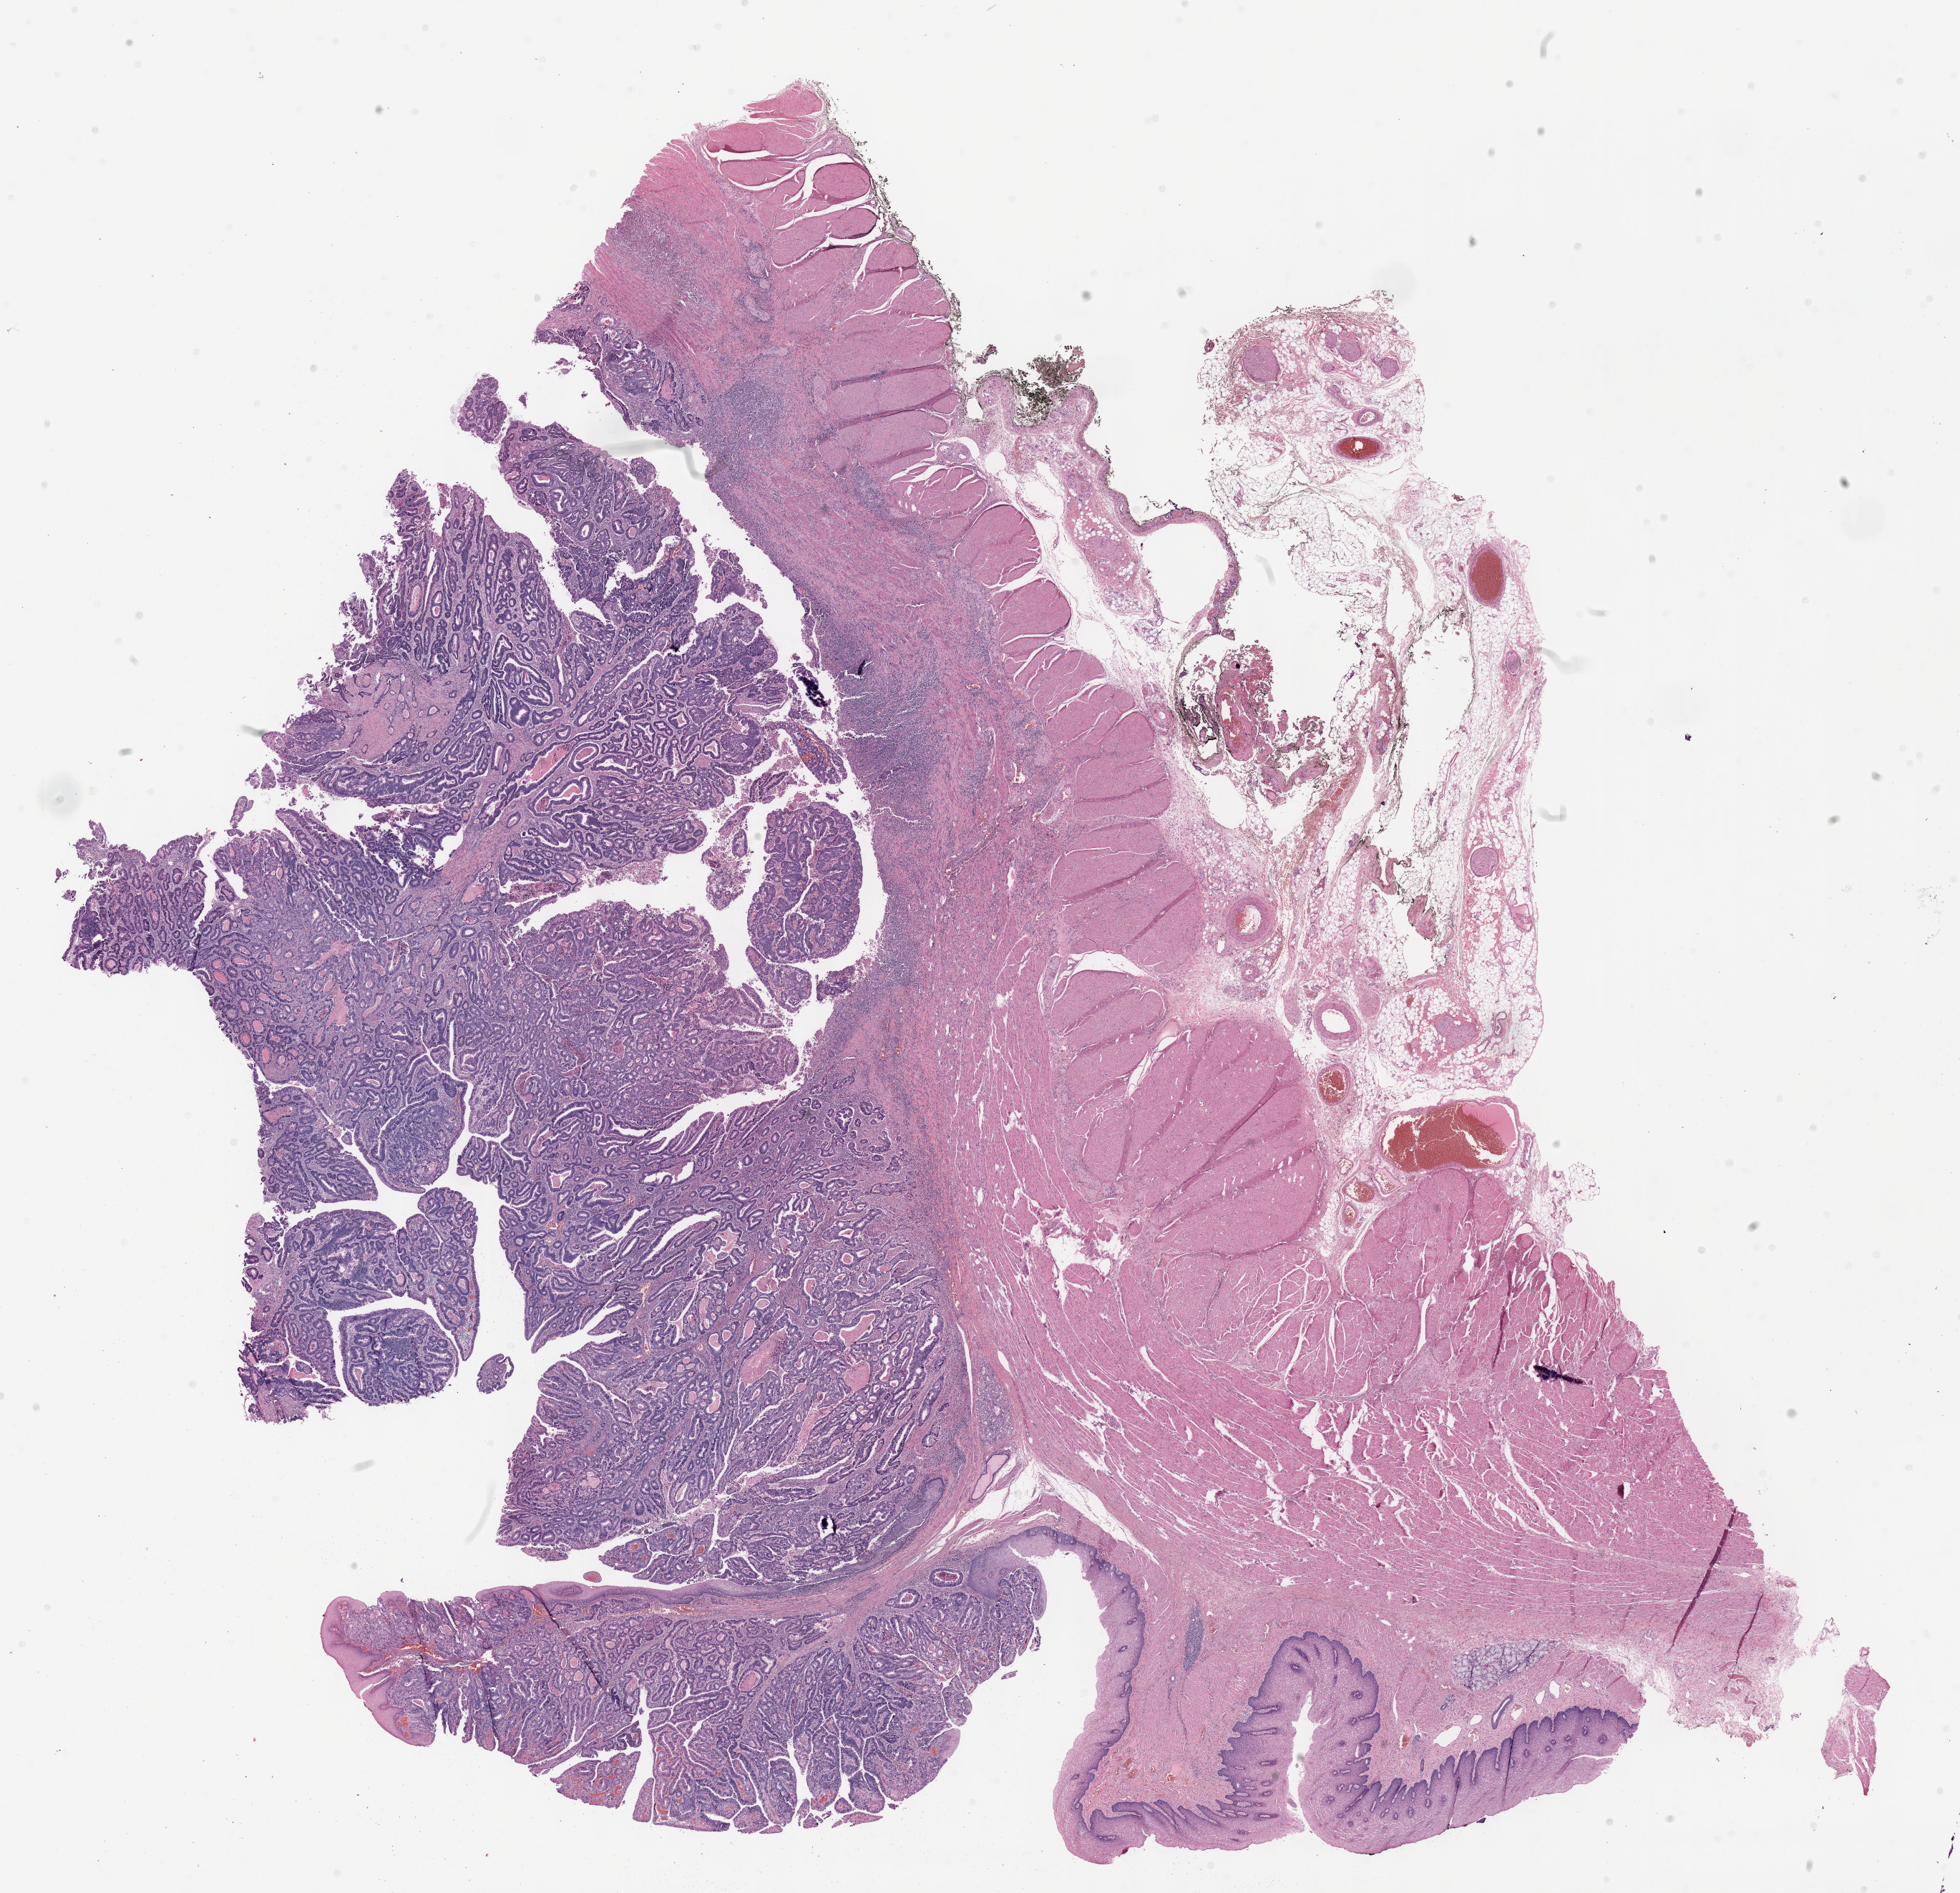
Digitized H&E tissue section (whole slide), whole scanned area (about 22.1 x 21.4 mm, acquisition: 40x scan) shown as a low-resolution overview; formalin-fixed paraffin-embedded (FFPE) diagnostic section; stomach, primary tumour sample. Male, age 48 years at initial diagnosis. Histologic grade: G2 (moderately differentiated).
• lymph nodes positive (case pathology): 5 of 39 examined
• pathologic diagnosis: Adenocarcinoma, intestinal type (cardia, NOS)
• AJCC pathologic stage: IIIB